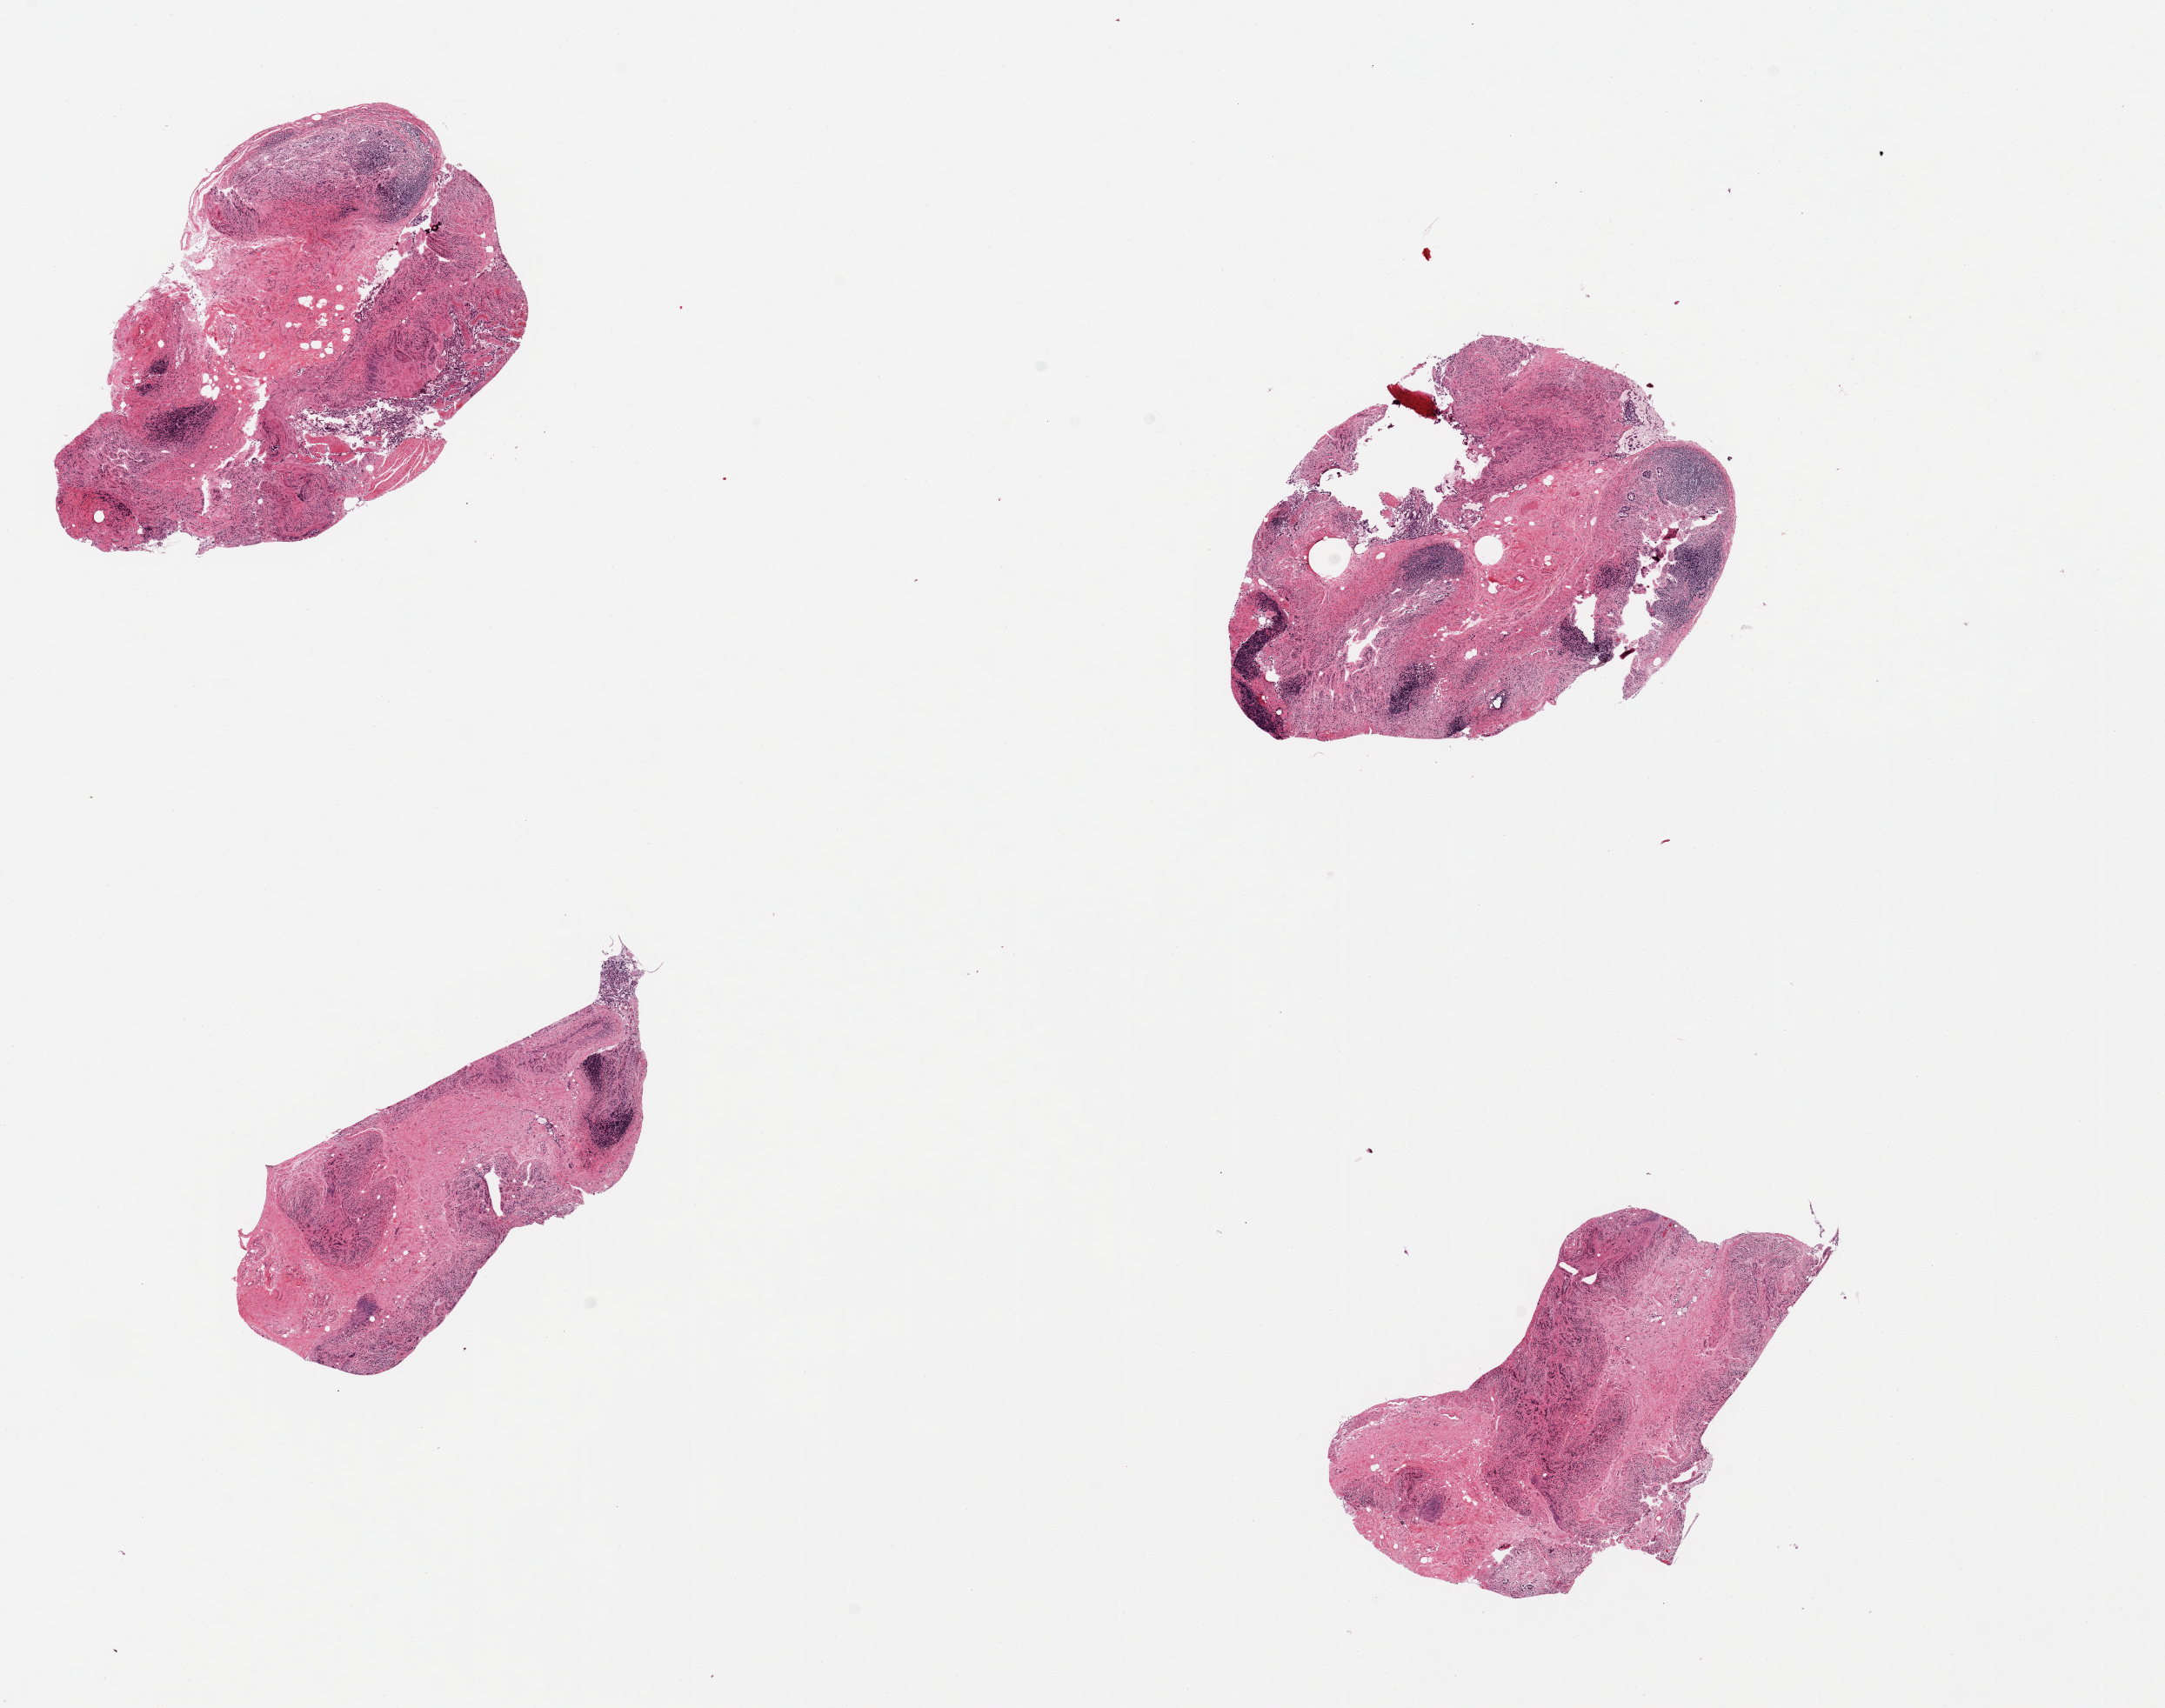
Digitized hematoxylin and eosin (H&E)-stained section, low-resolution overview of the scanned area, about 19.7 x 15.5 mm; PAXgene-fixed, paraffin-embedded tissue; section of ileum (target tissue); tissue donor sample. Donor sex: male.
Pathologist's review note for this sample: 4 pieces, 50% autolyzed mucosa, lymphoid aggregates well sampled, though; ~20% total area.